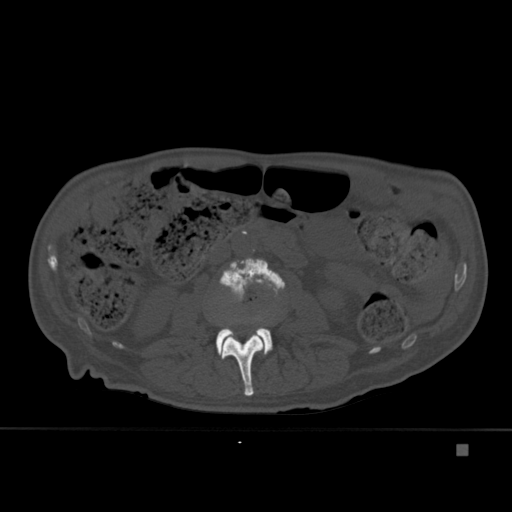
CT including the spine, one axial slice. Position 153 of 451 along the scan axis. Bone window (W 1800 / L 400 HU). 1.5 mm slice thickness. 512 × 512 image matrix. Patient: male, 75 years. Case-level facts recorded for this patient, not image findings: primary cancer: prostate.
Structures marked on this image (semi-automatic segmentation, software-assisted and operator-edited):
- L2 vertebra: box from (x=221, y=317) to (x=266, y=396) px
- L3 vertebra: (x=218, y=258)–(x=285, y=355)